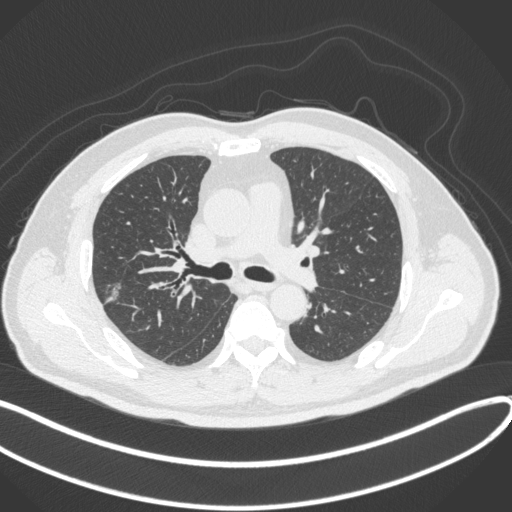
Chest CT, one axial slice; position 211 of 373 along the scan axis; 120 kVp; lung window (W 1500 / L -600 HU); 512 × 512 image matrix, field of view 400 × 400 mm. Male patient, age 60 years. Case-level facts recorded for this patient, not image findings: clinical TNM (as recorded): T1c N0 M0.
Outlined on this slice (bounding box drawn by a radiologist):
- lung tumour (recorded histology: adenocarcinoma): box from (x=98, y=275) to (x=126, y=311) px